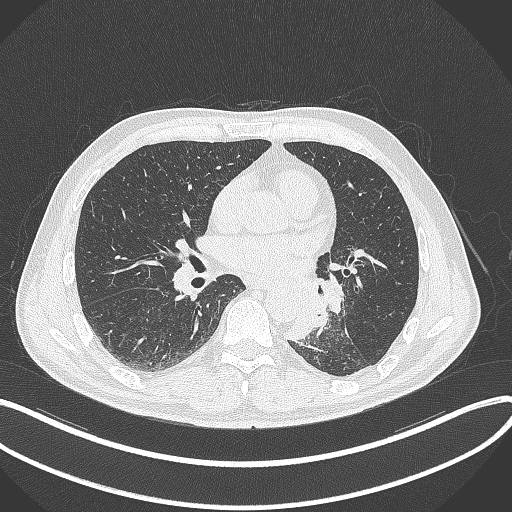
Chest CT, one axial slice. Reconstruction kernel B70f. Lung window (W 1500 / L -600 HU). 512 × 512 image matrix. Male patient, age 59 years. Case-level facts recorded for this patient, not image findings: clinical TNM (as recorded): T2a N2 M0.
Structures marked on this image (bounding box drawn by a radiologist):
- lung tumour (recorded histology: squamous cell carcinoma): bounding box (x1, y1, x2, y2) in pixels: (285, 287, 329, 345)